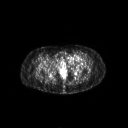
FDG PET of an extremity soft-tissue mass (from a PET/CT study), one axial slice; position 48 of 267 along the scan axis; 3.27 mm slice thickness; 128 × 128 image matrix, field of view 700 × 700 mm. Patient: female, 47 years. From the clinical record (not read from this slice): histological type: myxofibrosarcoma; grade: intermediate; site of the primary tumour: left thigh.
Annotated regions visible in this slice (expert contour drawn on MRI and transferred to this co-registered scan by the dataset authors):
- gross tumour volume including surrounding oedema: bounding box [x1, y1, x2, y2] px = [65, 55, 83, 63]